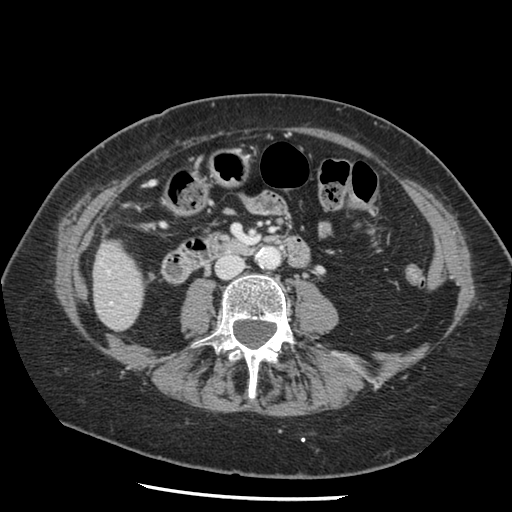
Contrast-enhanced abdominal CT, one axial slice. Slice 26 of 148 in the series (ordered by position). 120 kVp. Intravenous contrast given. Soft-tissue window (W 400 / L 40 HU). 2.5 mm slice thickness. 512 × 512 image matrix, field of view 330 × 330 mm. Female patient, age 85 years. Case-level facts recorded for this patient, not image findings: diagnosis: colorectal cancer liver metastases, imaged before liver resection; multiple liver metastases: no; largest metastasis: 0.9 cm; disease in both lobes: no.
Outlined on this slice (outlined manually by an expert reader):
- liver: bounding box (x1, y1, x2, y2) in pixels: (94, 242, 144, 330)
- planned liver remnant (the part of the liver to remain after resection): (94, 242, 144, 330)